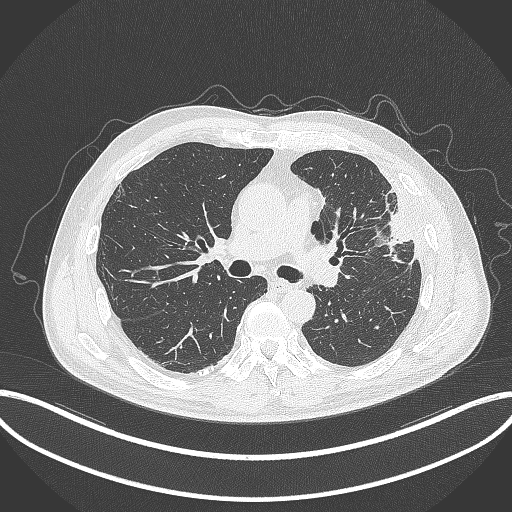
Chest CT, one axial slice. Slice 200 of 382 in the series (ordered by position). Lung window (W 1500 / L -600 HU). 1 mm slice thickness. 512 × 512 image matrix, field of view 415 × 415 mm. Patient: male, 64 years. From the clinical record (not read from this slice): clinical TNM (as recorded): T4 N1 M0; histopathological grade: G3.
Outlined on this slice (rectangle marked by the reading radiologist):
- lung tumour (recorded histology: adenocarcinoma): bounding box [x1, y1, x2, y2] px = [374, 180, 416, 262]